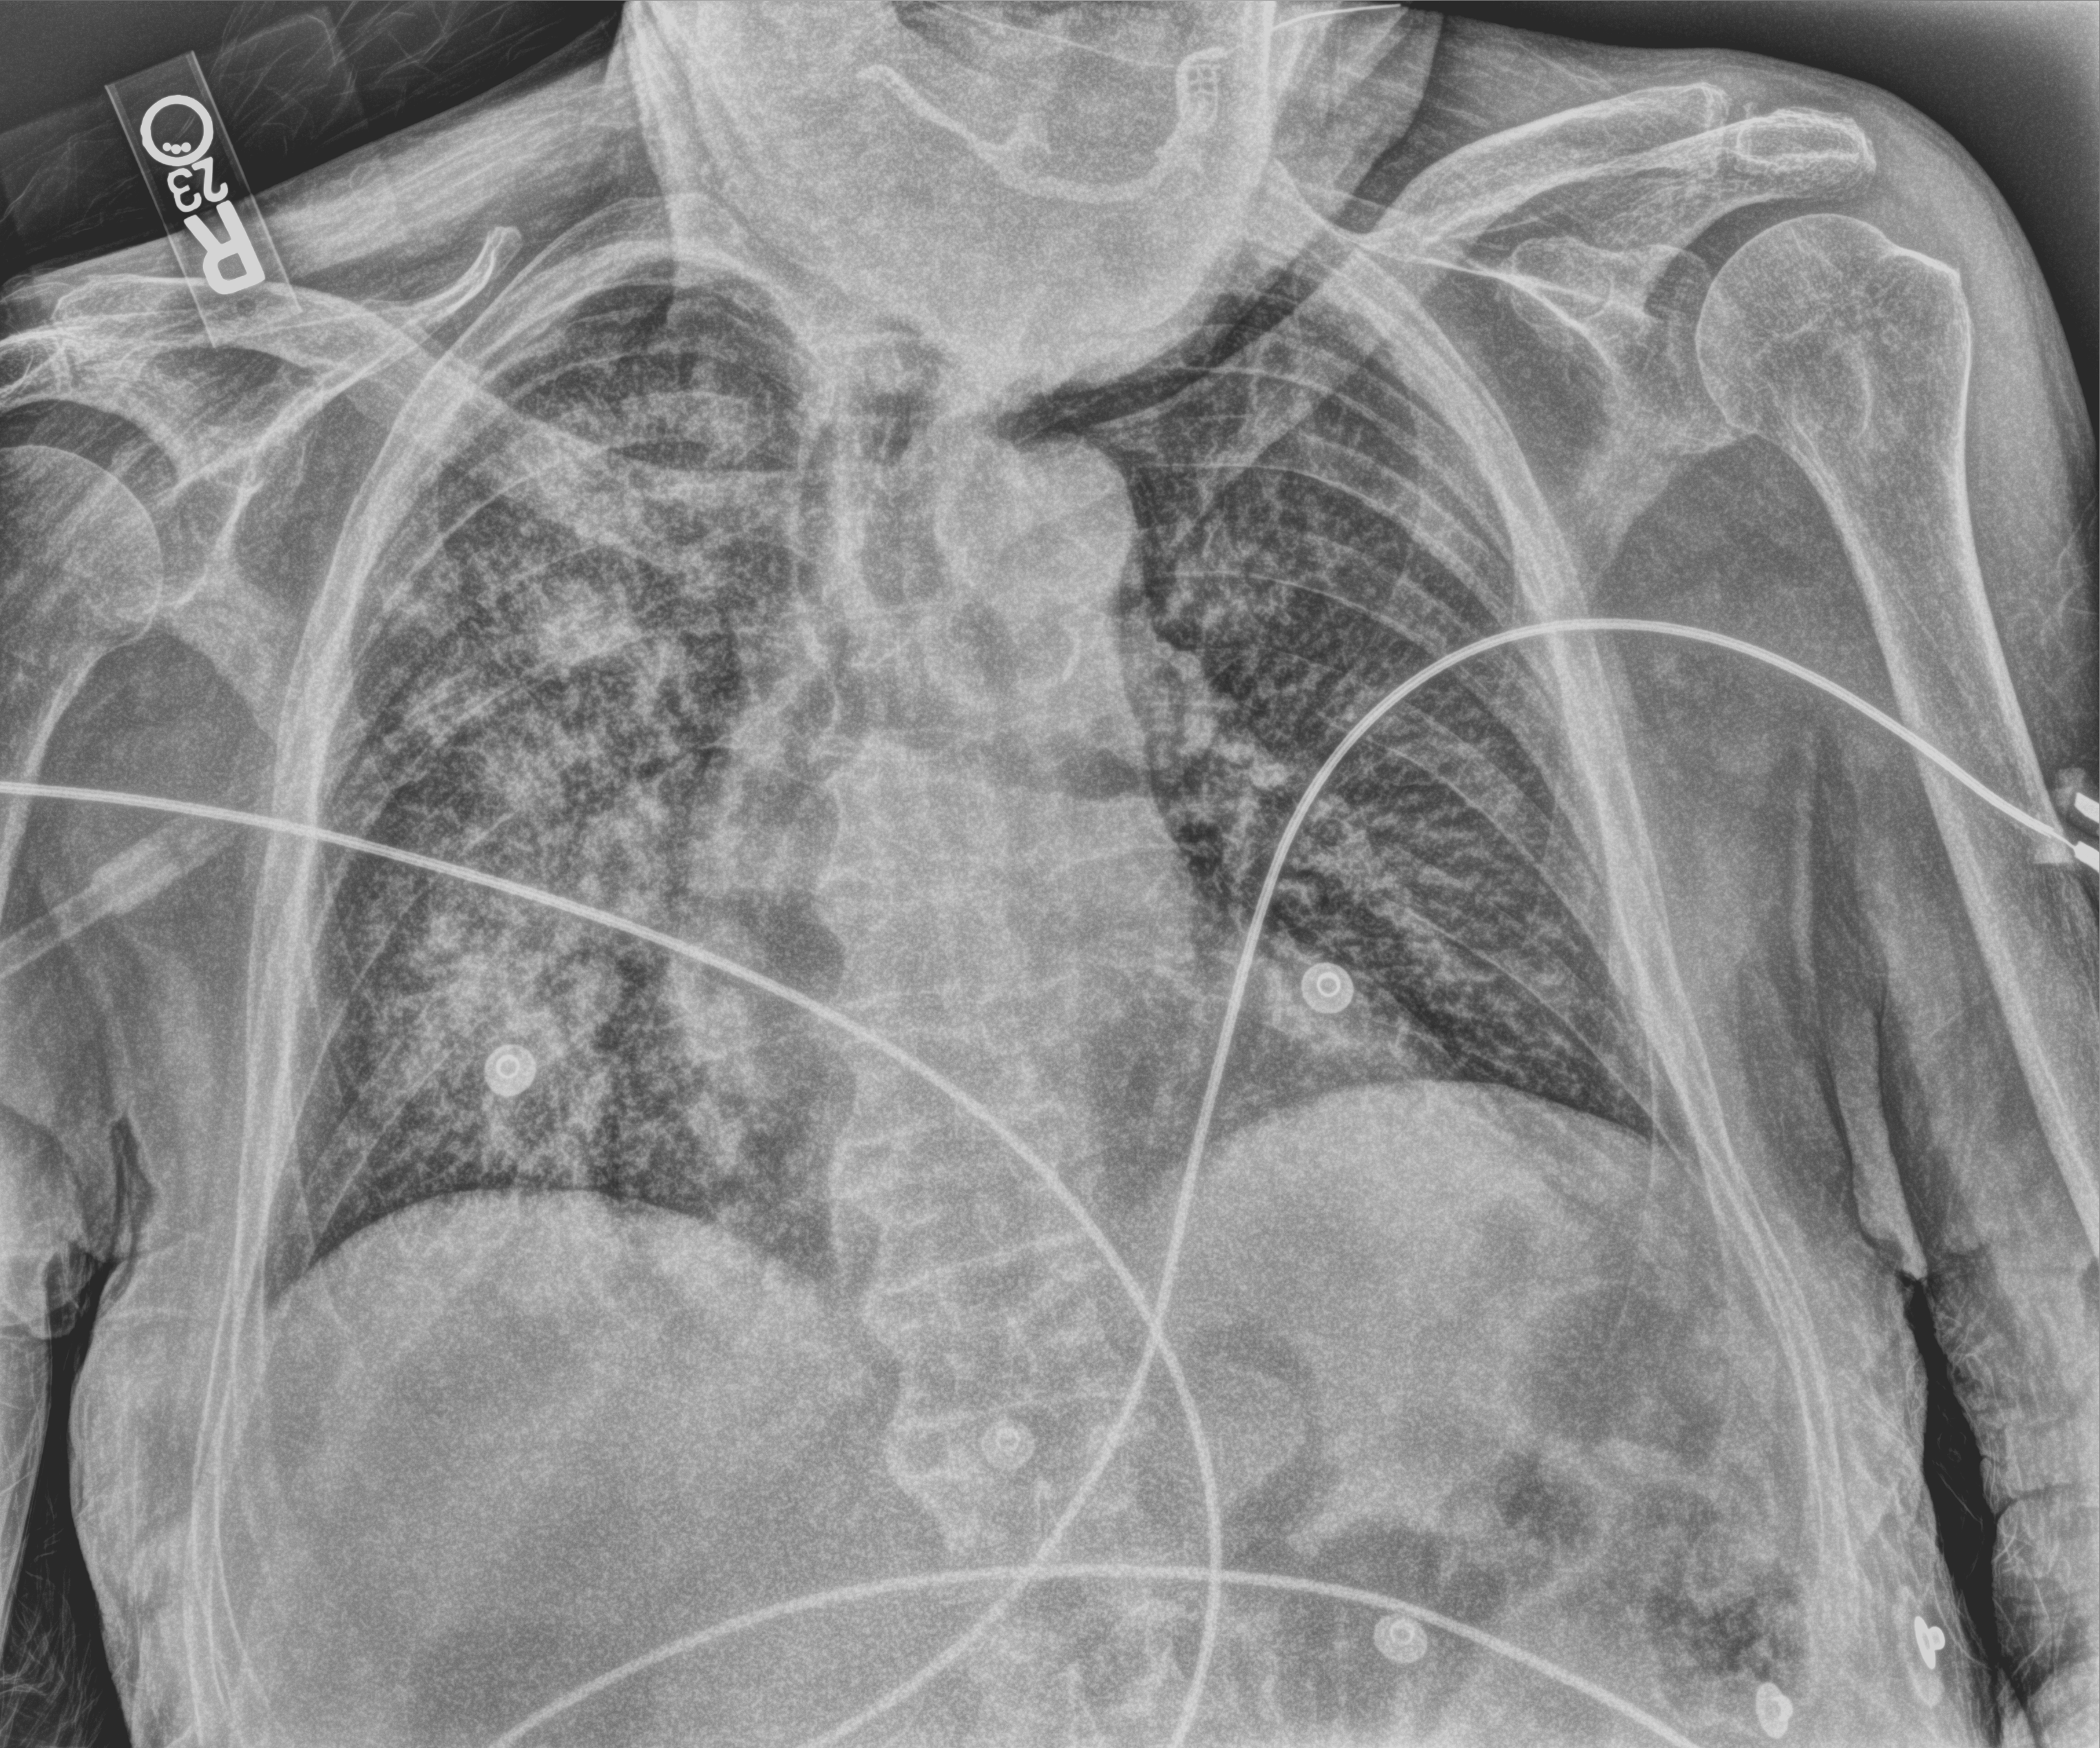
Chest X-ray (portable), anteroposterior (AP) projection. Patient hospitalised with COVID-19; male, aged 75–90 years.
From the hospital-stay record, not from the radiograph (when in the stay this image was taken is not recorded): admitted to intensive care during this hospital stay: no.